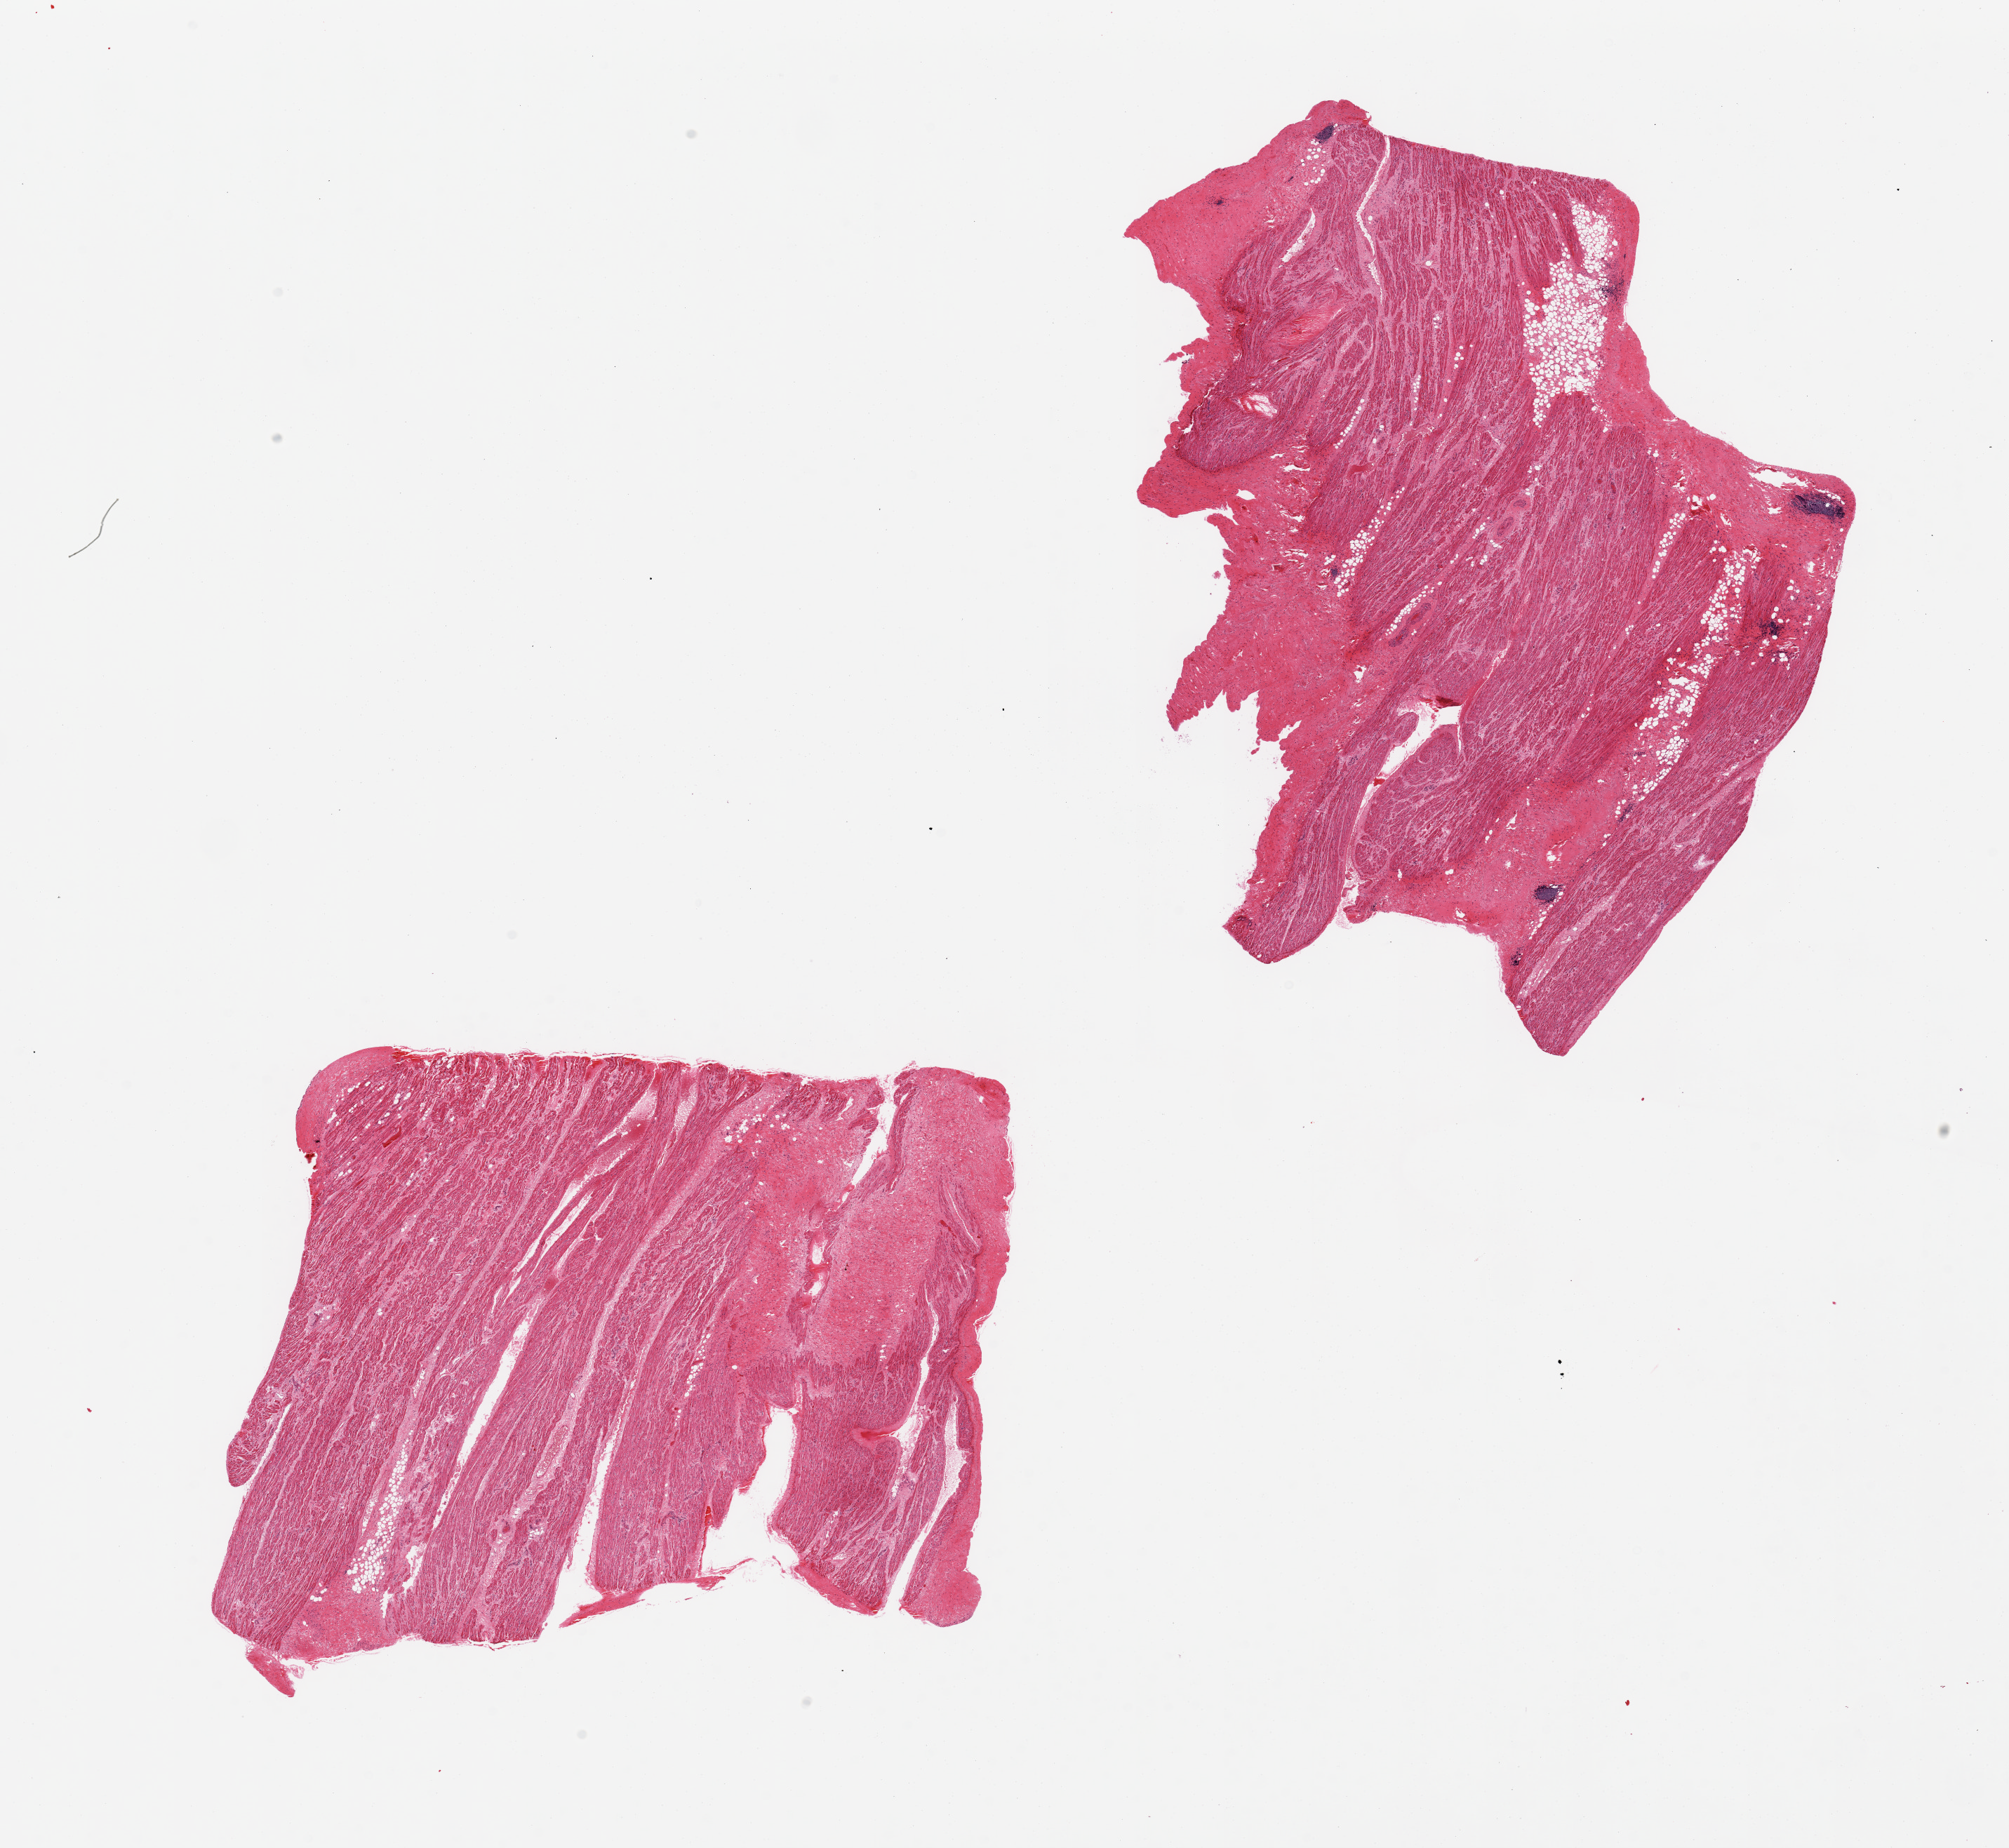
Digitized H&E-stained section — whole scanned area (about 22.6 x 20.8 mm) shown as a low-resolution overview; PAXgene-fixed paraffin-embedded (PFPE) section; target tissue: auricular appendage; donor tissue sample. Donor: male.
Pathologist's review note for this sample: 2 pieces, no abnormalities.